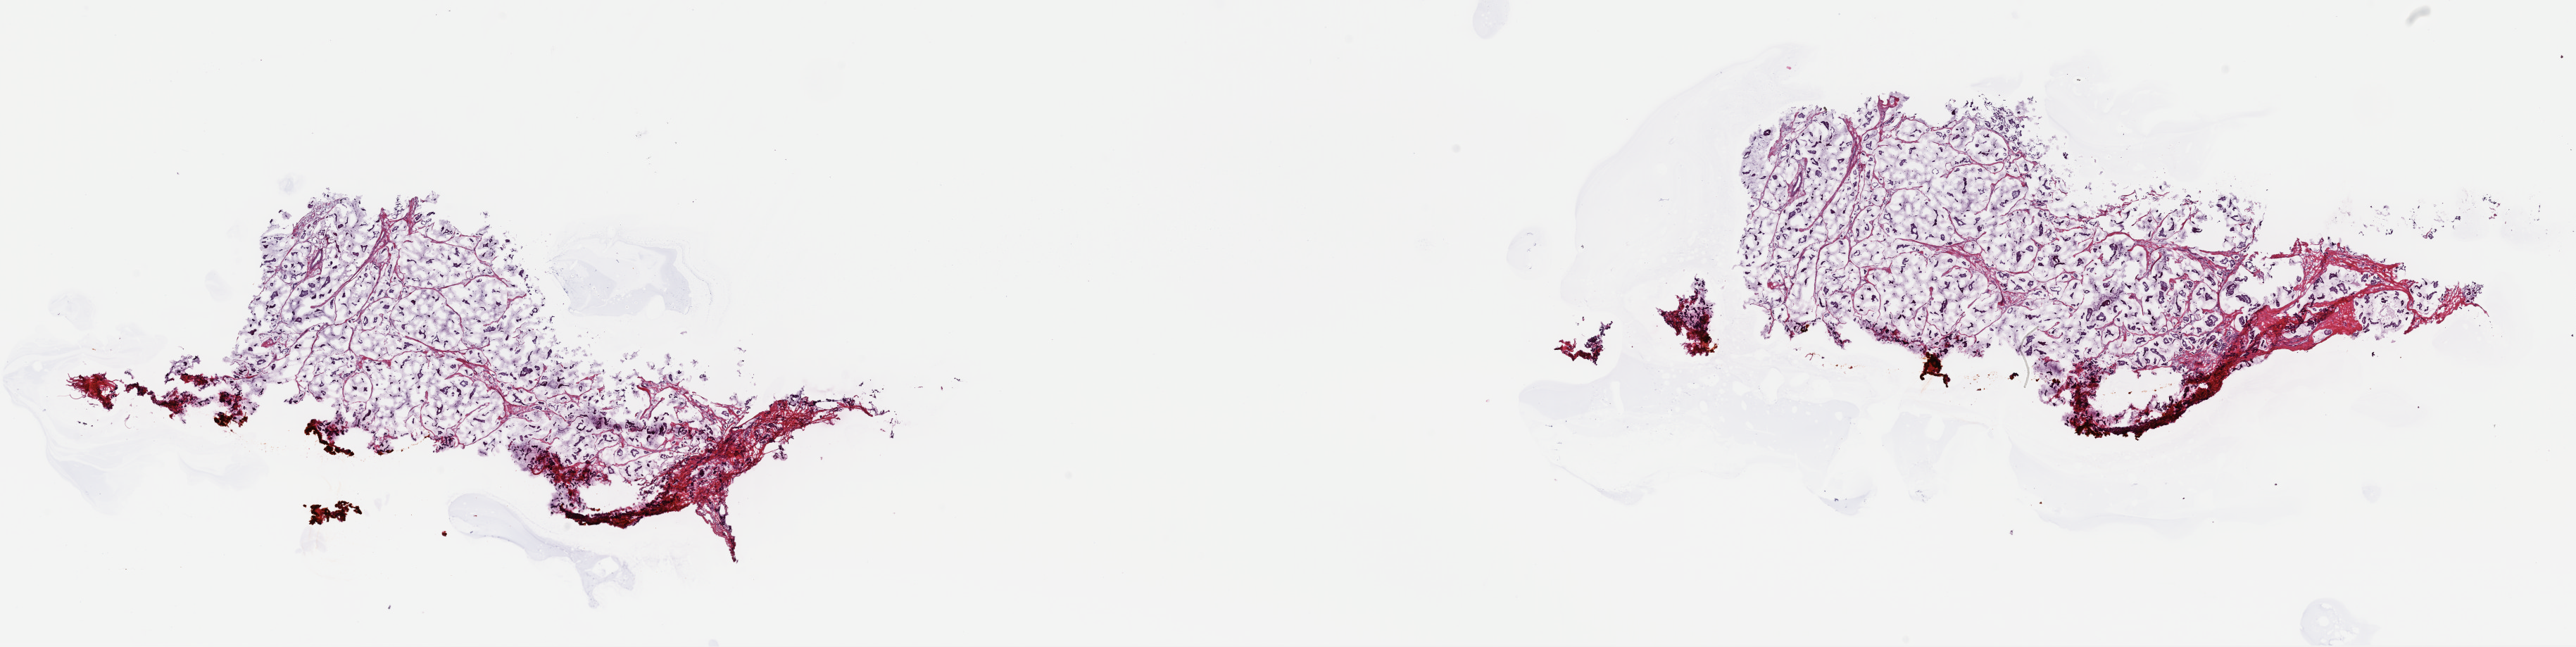
Whole-slide histology image, Hematoxylin and eosin (H&E) stained, low-resolution overview of the scanned area, about 28.9 x 7.3 mm (from a 40x scan); frozen section from the top of the tissue portion; sample: primary tumour, breast. Patient: female, age at initial diagnosis 47 years. Composition of this section per pathologist review: tumour cells 100%, tumour nuclei 90%, normal cells 0%, stromal cells 0%, necrosis 0%. Infiltration values recorded for this section: lymphocyte infiltration 0%, monocyte infiltration 0%, neutrophil infiltration 0%.
Laterality: right. AJCC pathologic stage: IIIA (7th edition). Diagnosis: Mucinous adenocarcinoma.